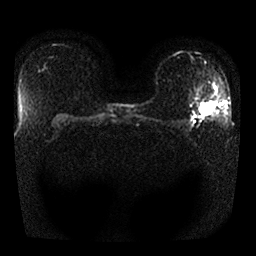
Breast MRI, one axial slice. Slice 18 of 25 in the series (ordered by position). Diffusion-weighted series; image 2 of 4 stored at this slice position (different b-values; order by instance number). 1.5 T. 256 × 256 image matrix. Female patient.
Annotated regions visible in this slice (outlined manually by an expert reader):
- tumour on diffusion-weighted imaging: box from (x=199, y=103) to (x=211, y=115) px